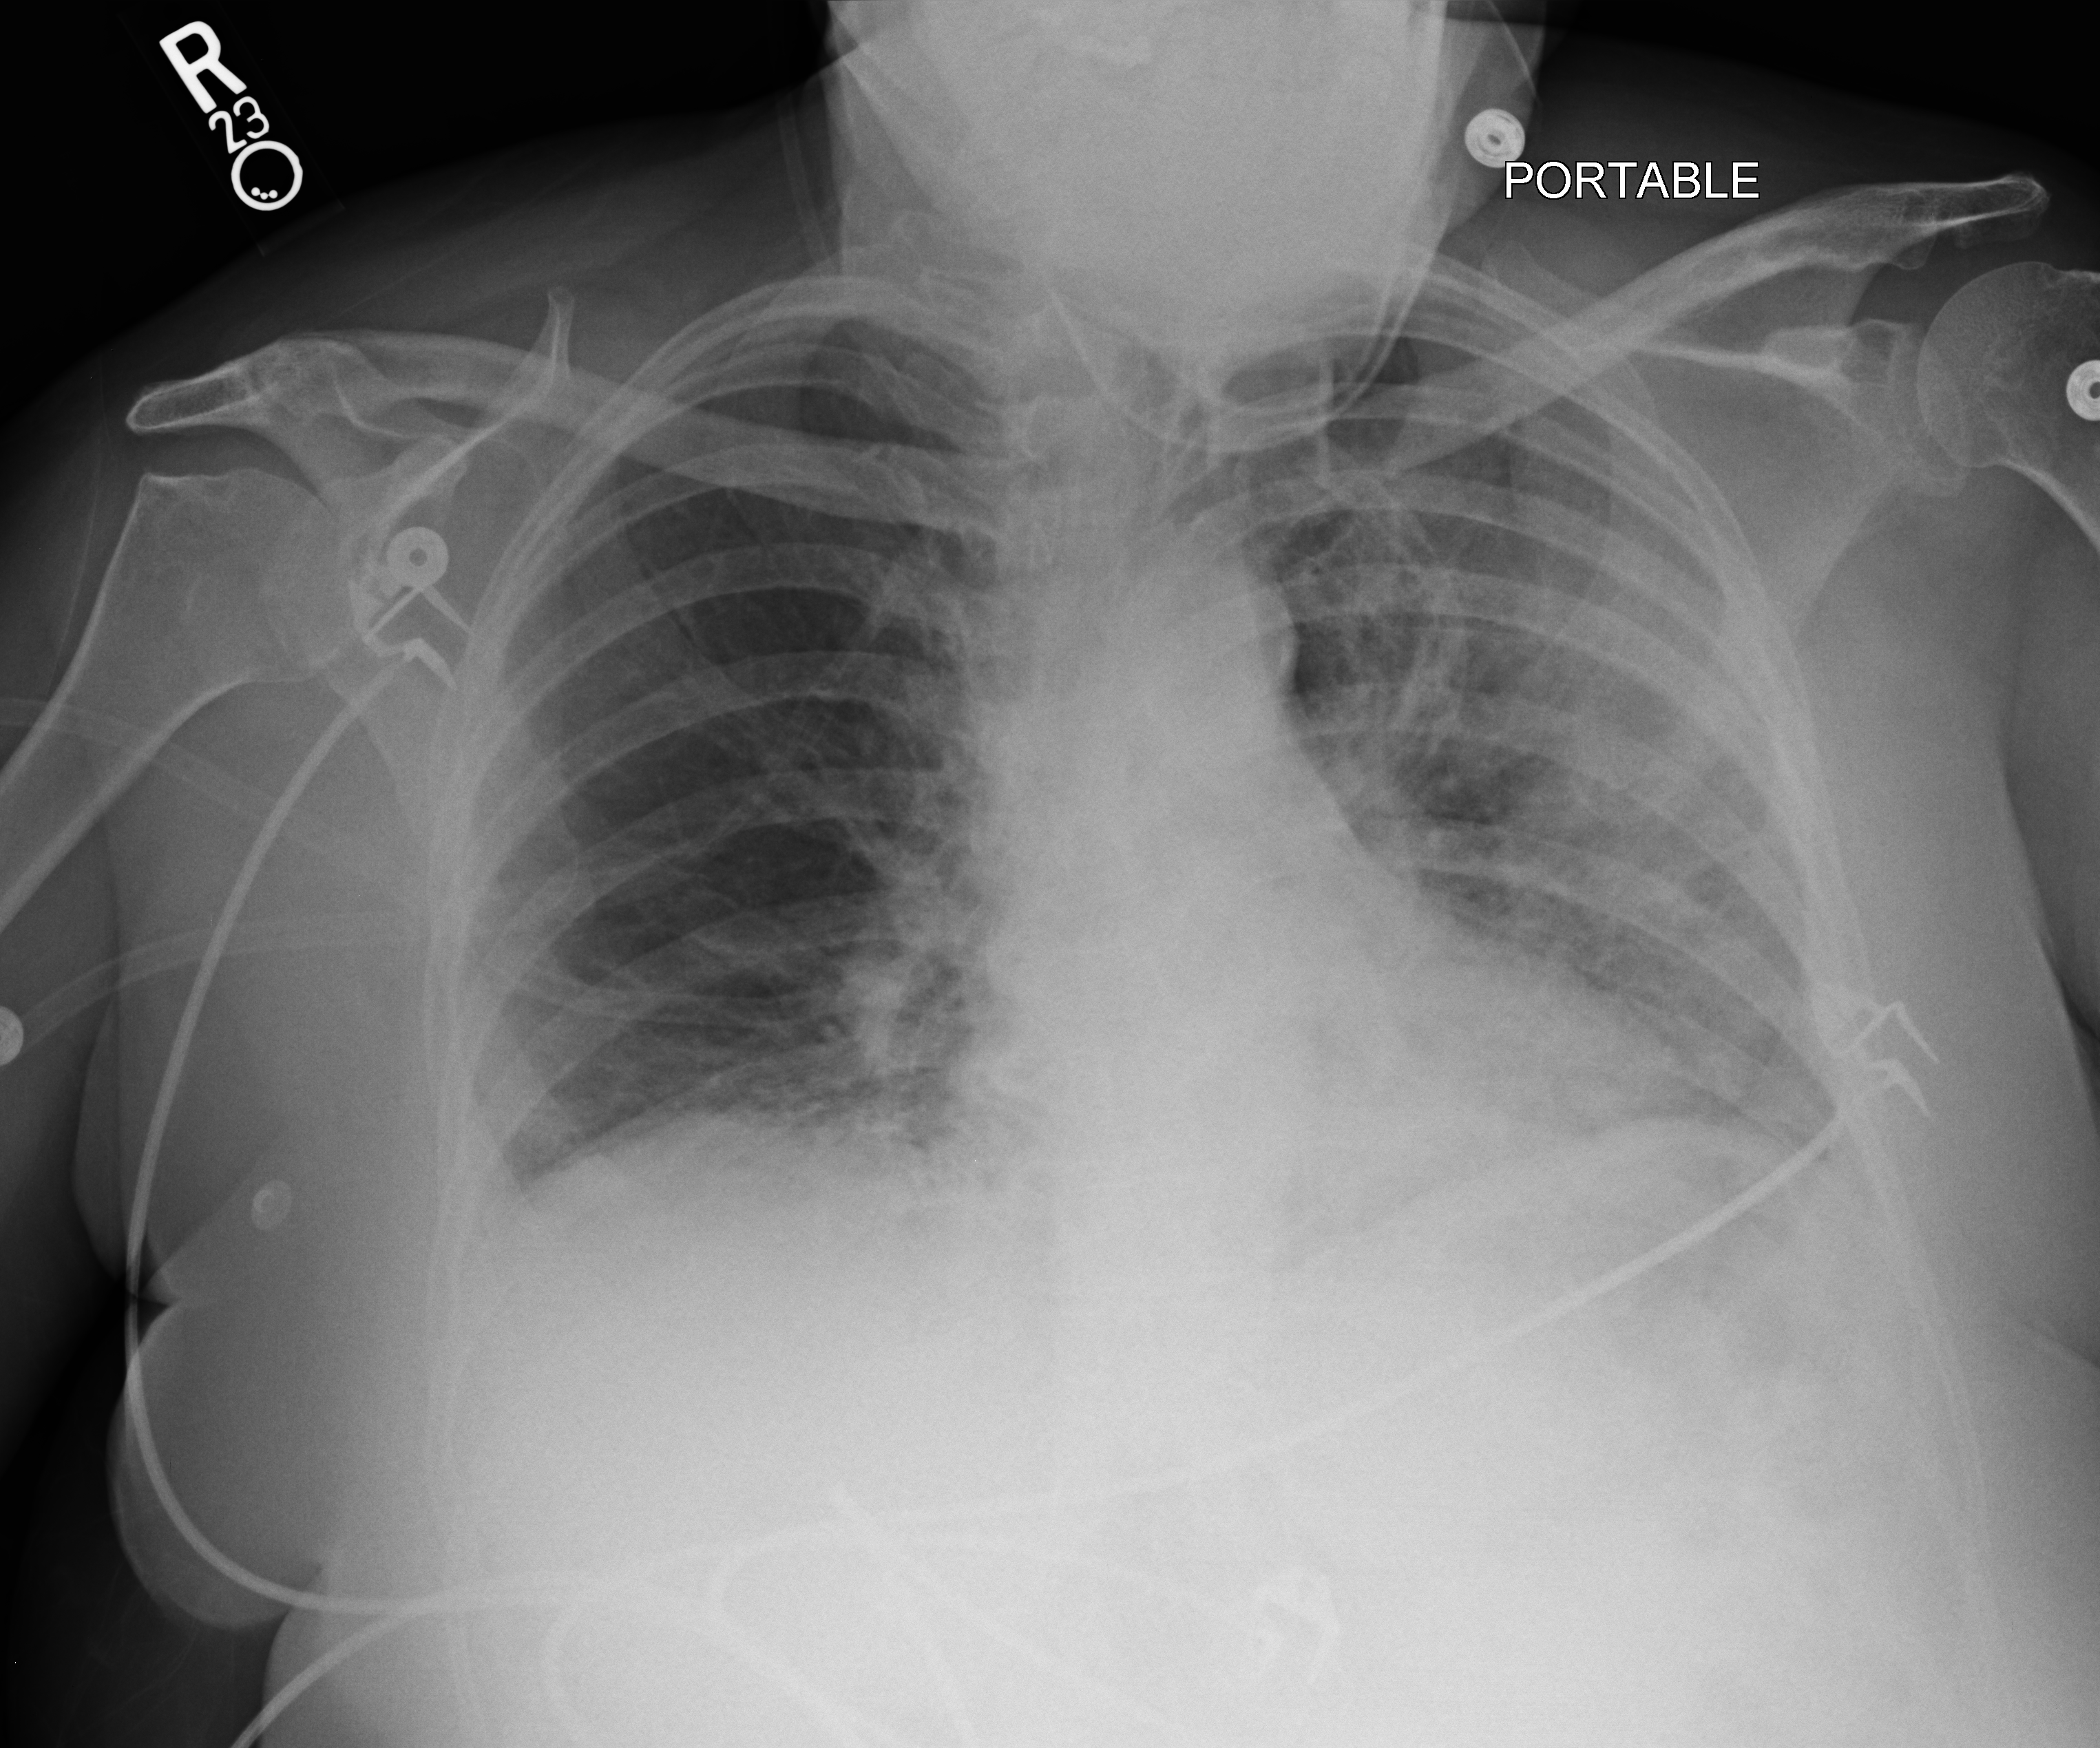
Portable chest radiograph. Patient hospitalised with COVID-19; female, aged 60–74 years.
Admission-level facts for this patient (not findings on this image; timing relative to this image not recorded): mechanically ventilated during this hospital stay: no; admitted to intensive care during this hospital stay: no.